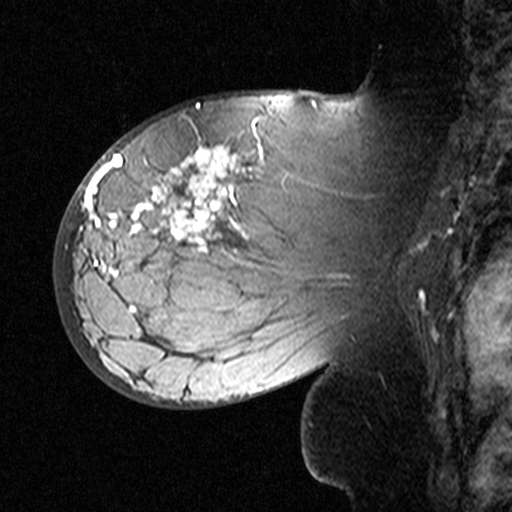
Breast MRI (dynamic contrast-enhanced), one sagittal slice; slice 27 of 44 in the series (ordered by position); dynamic contrast-enhanced study with each time point stored as its own series, time point 2 of 3 at this slice position (early post-contrast, ordered by acquisition time); 1.5 T; TE 4.5 ms, TR 11 ms; 3 mm slice thickness; 512 × 512 image matrix, field of view 200 × 200 mm. Female patient, age 53 years. From the clinical record (not read from this slice): setting: breast cancer imaged before/during neoadjuvant chemotherapy; receptor status: HR-positive, HER2-negative.
Outlined on this slice (semi-automatically segmented with operator editing):
- analysis volume of interest (the breast-tissue region the enhancement analysis was run in; not a lesion): bounding box <76,140,311,353> (left, top, right, bottom; pixels)
- tumour enhancement mask (voxels above the 90 % enhancement threshold inside the analysis volume of interest): <95,145,264,308>